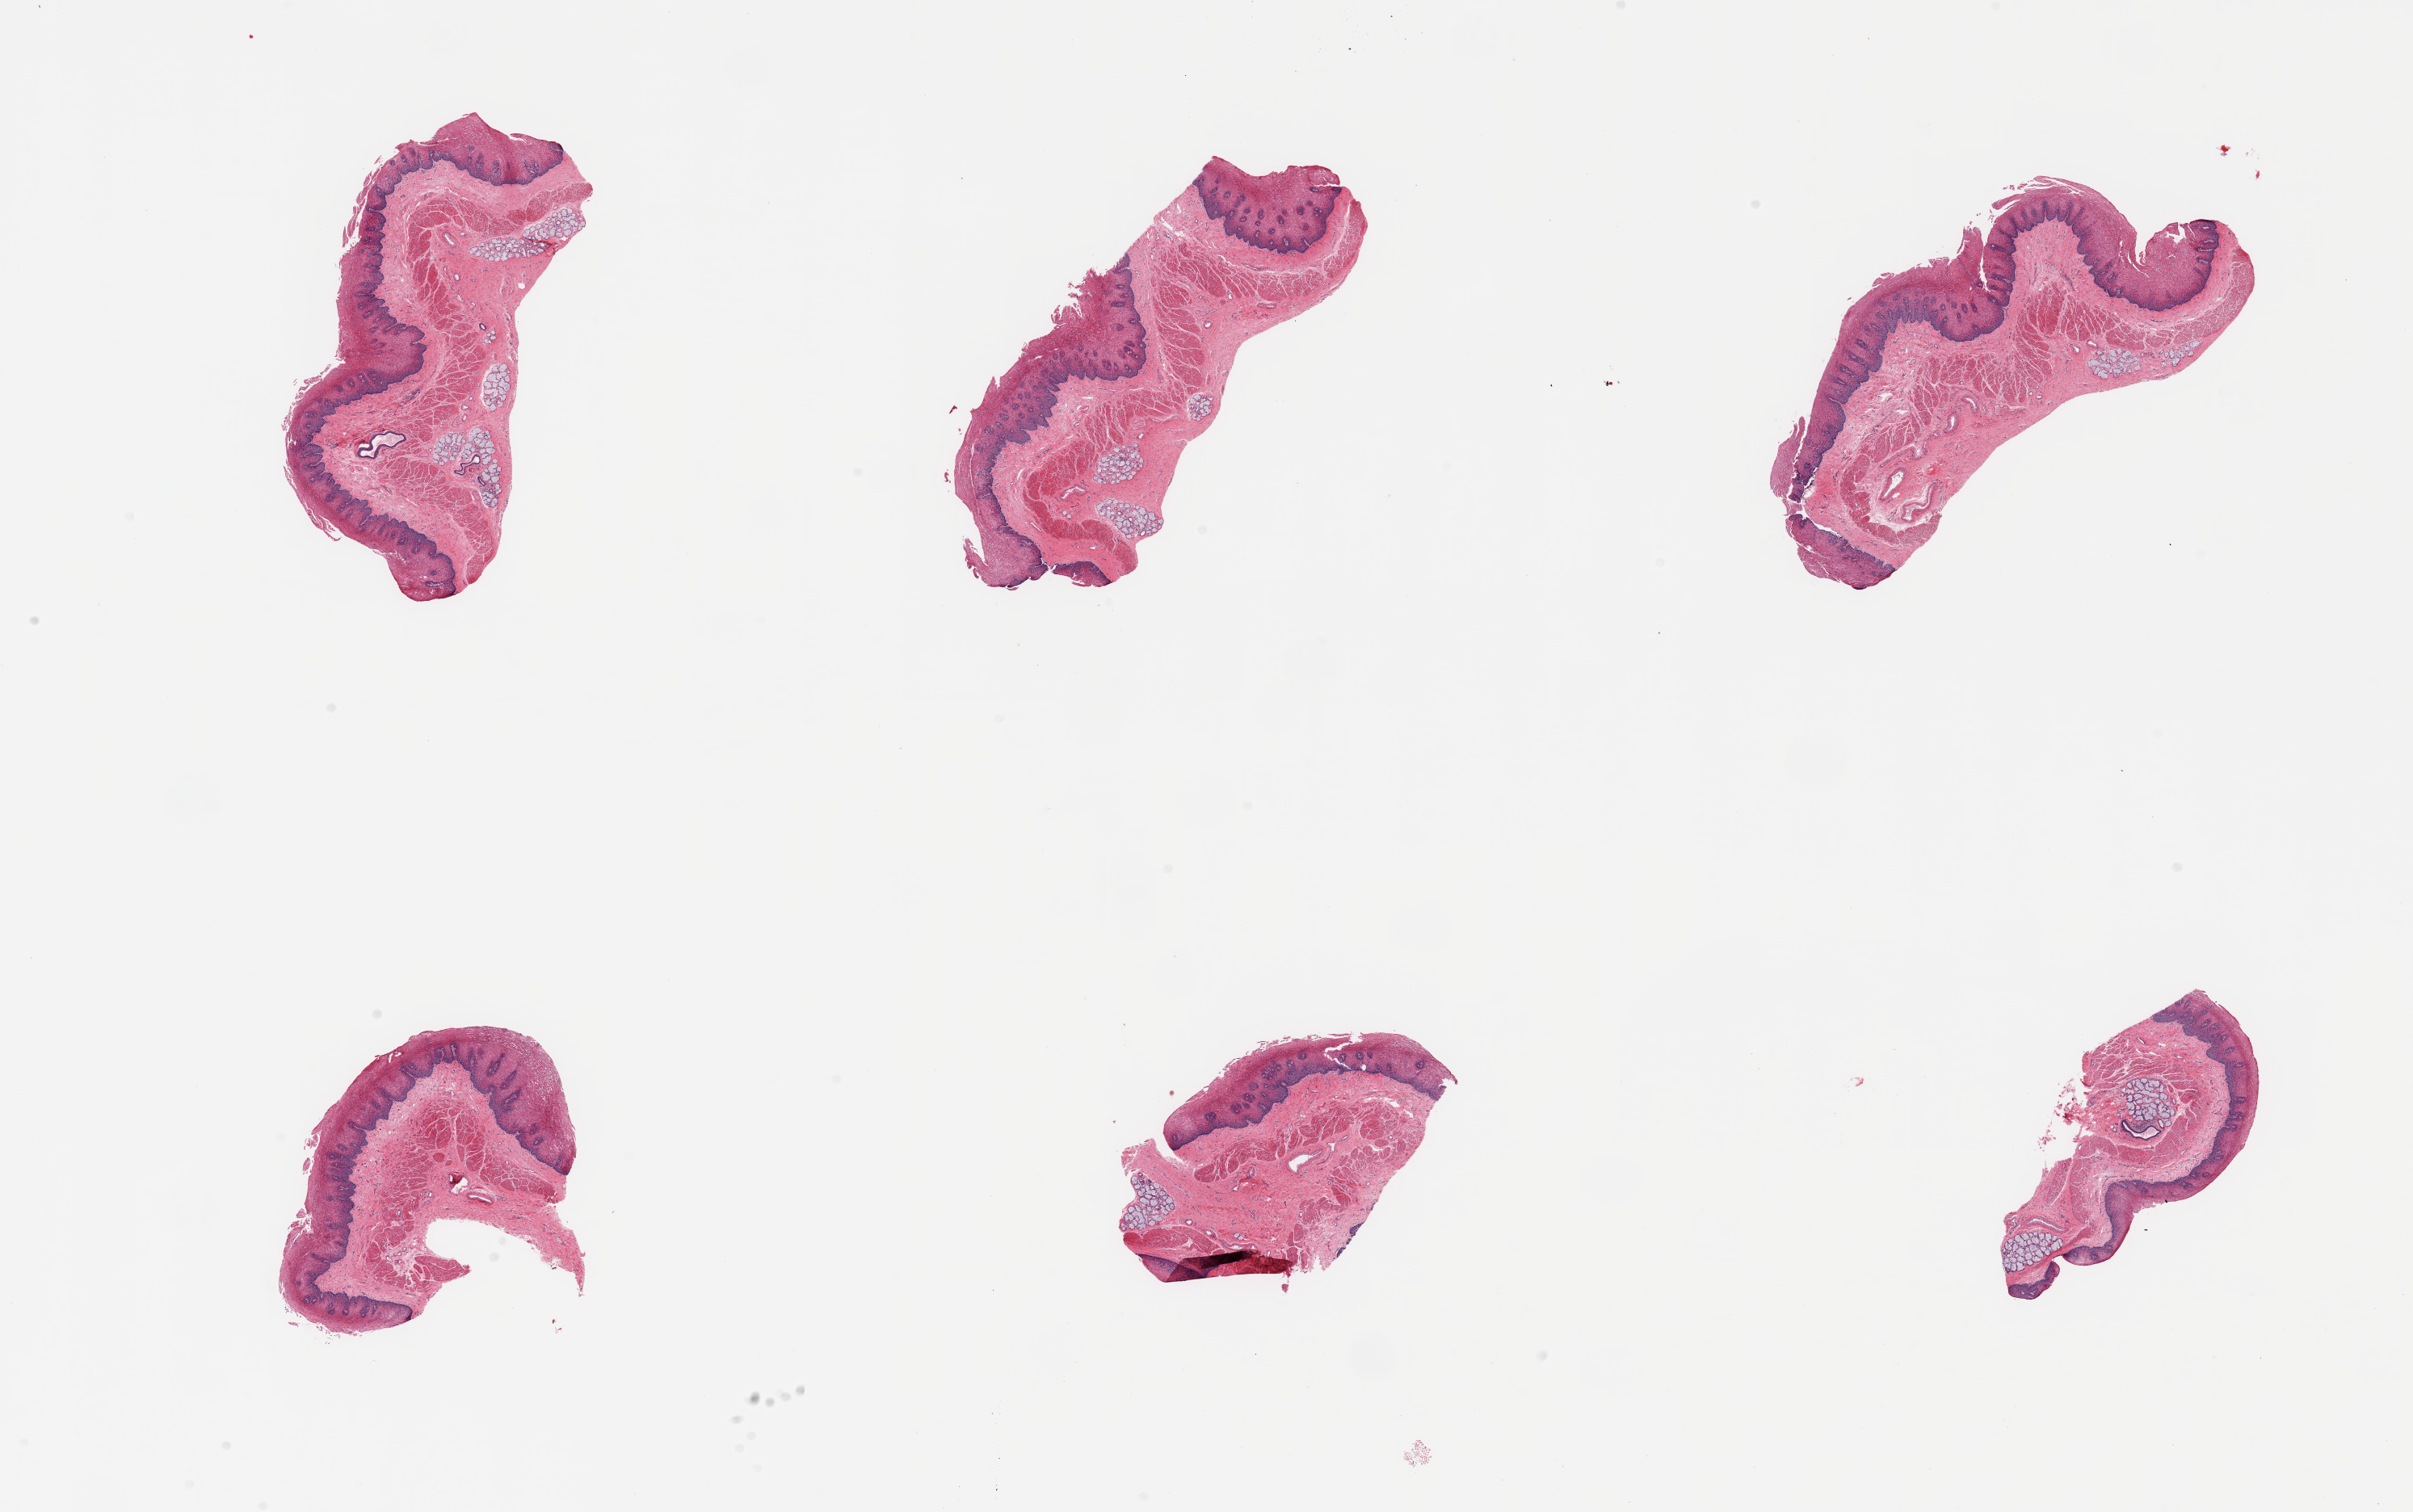
Whole-slide image, H&E stain — a low-resolution overview of the entire scanned area, about 23.6 x 14.8 mm (acquisition: 20x scan). PAXgene-fixed paraffin-embedded (PFPE) section. Target tissue: esophageal mucous membrane. Tissue donor sample. Donor sex: male.
Review note (as recorded): 6 pieces, squamous mucosa up to ~0.5mm, submucosal mucusa glands present.